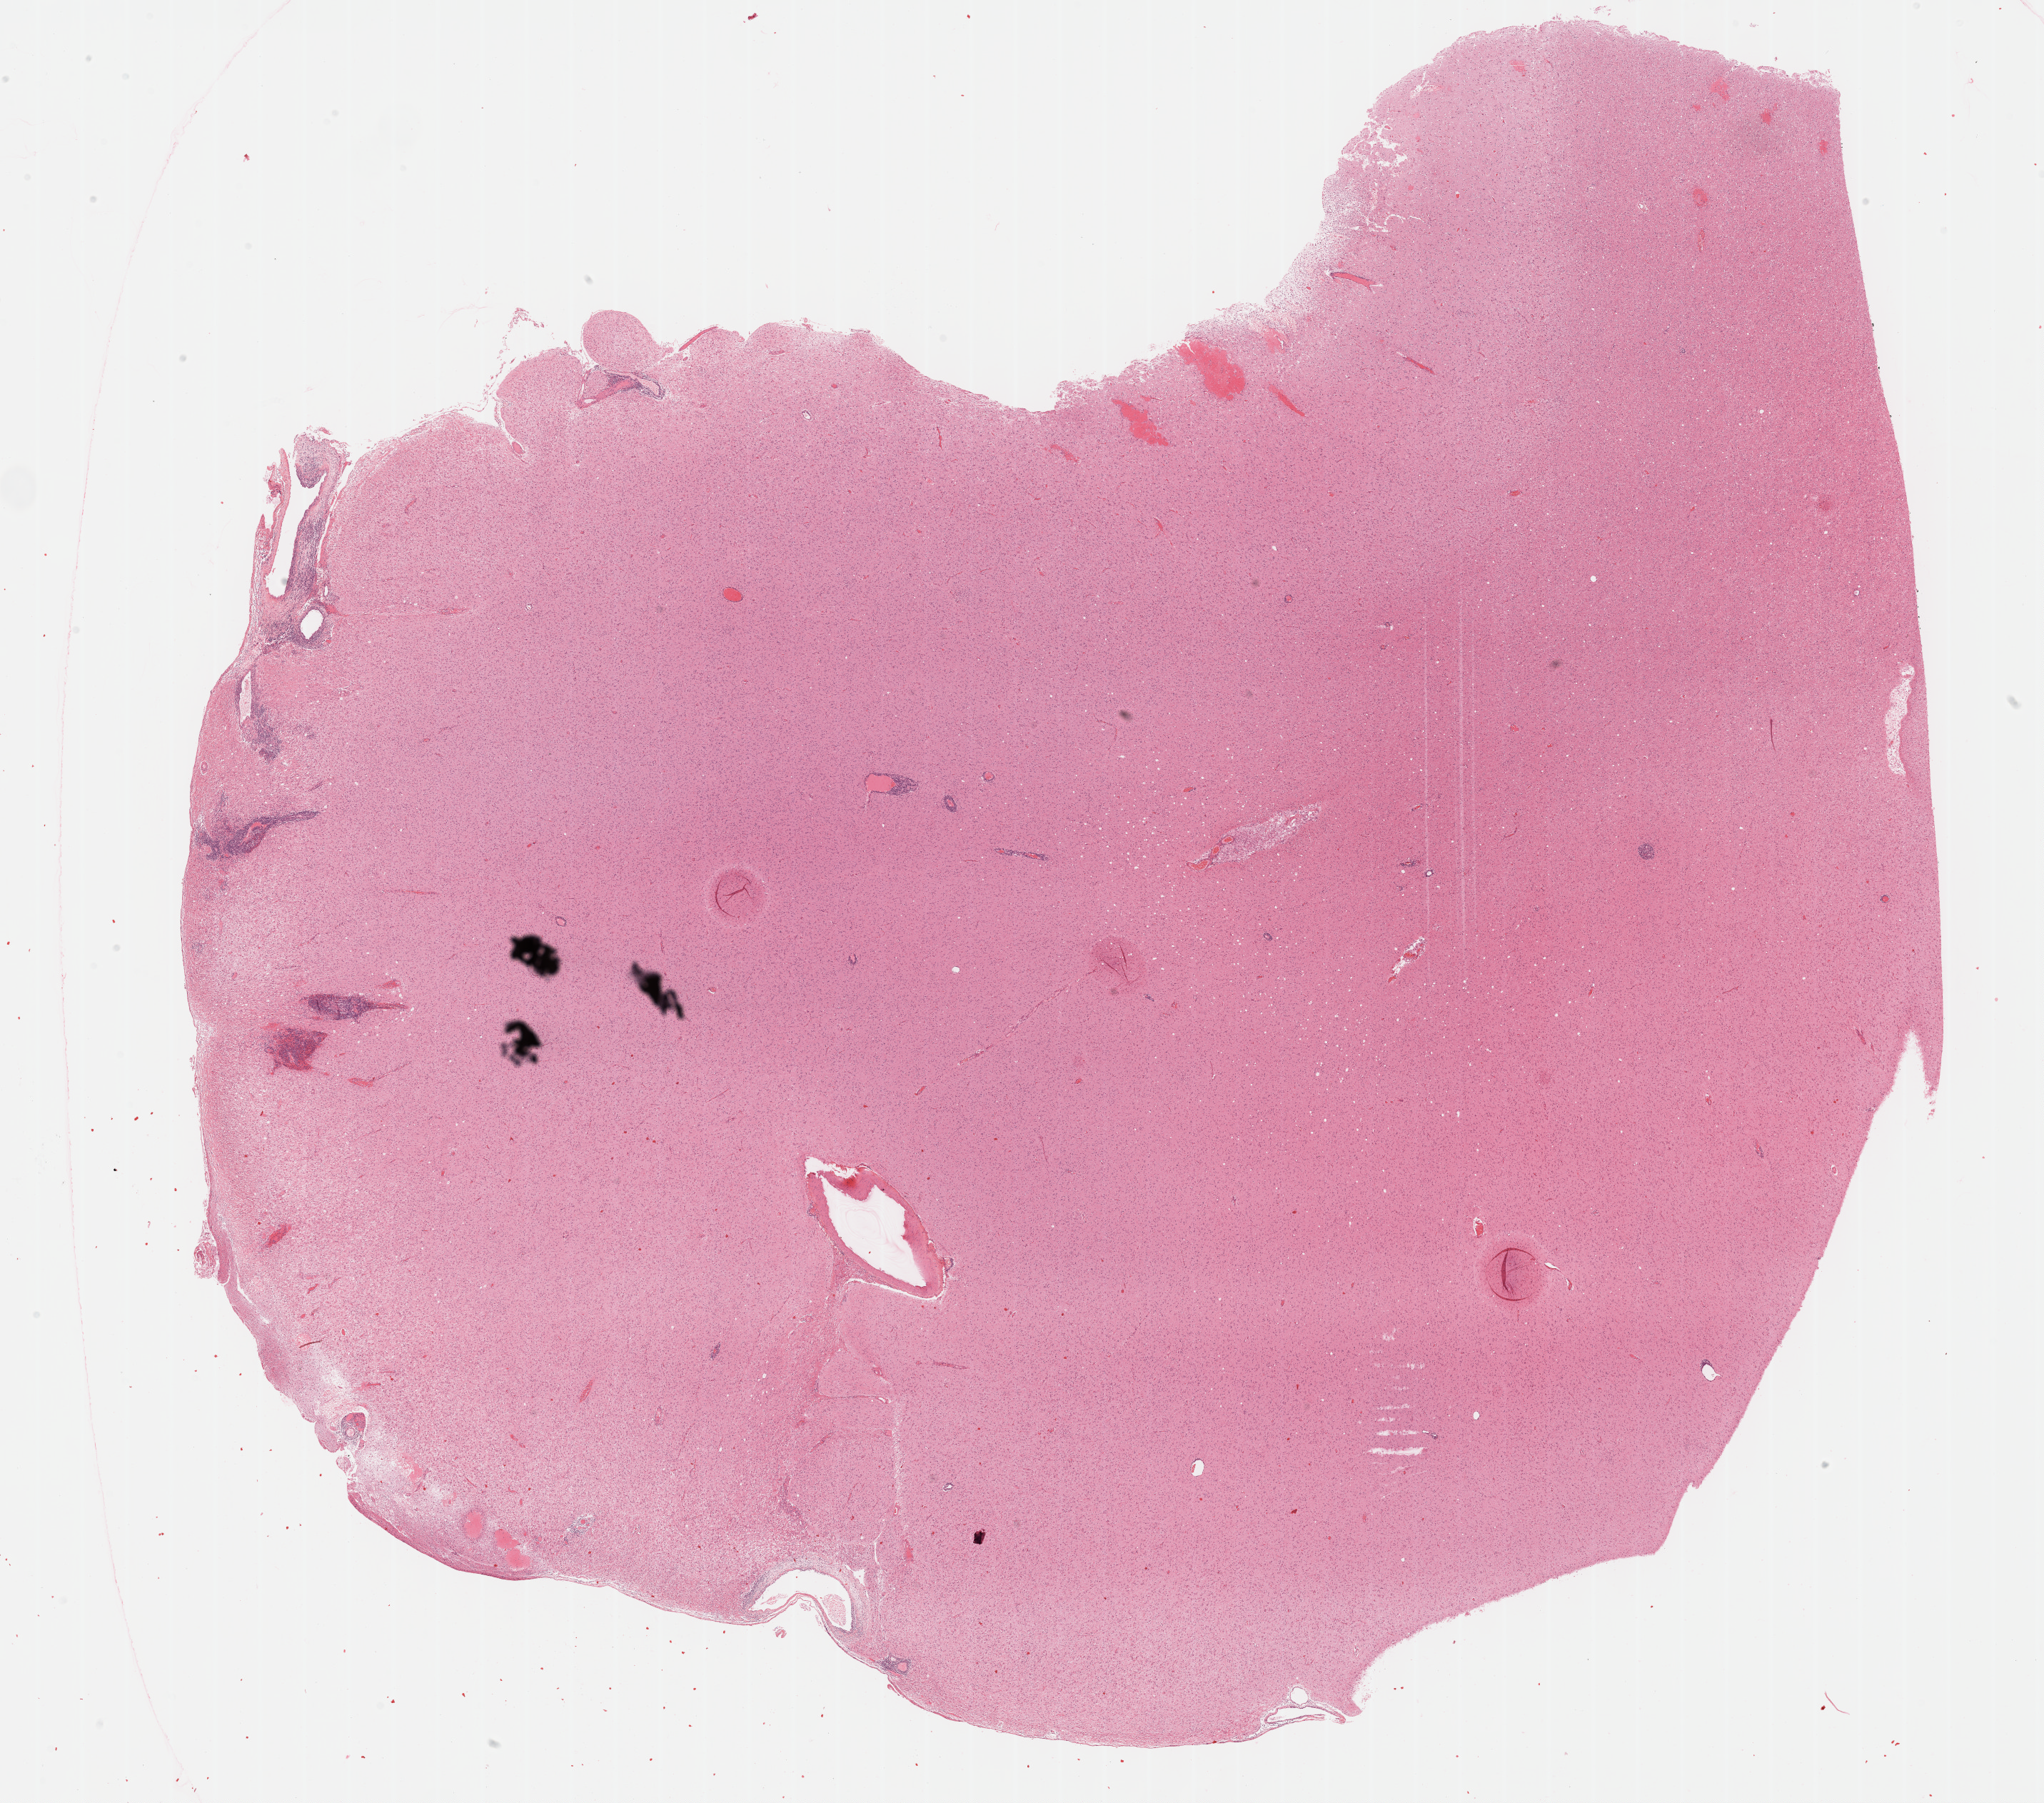
Digitized H&E tissue section (whole slide) — whole scanned area (about 23.2 x 20.4 mm, acquisition: 40x scan) shown as a low-resolution overview; formalin-fixed paraffin-embedded (FFPE) diagnostic section; sample: primary tumour, brain. Male patient; age at initial diagnosis 48 years. Histologic grade: G3 (poorly differentiated).
Pathologic diagnosis: Astrocytoma, anaplastic (cerebrum). Laterality: right.